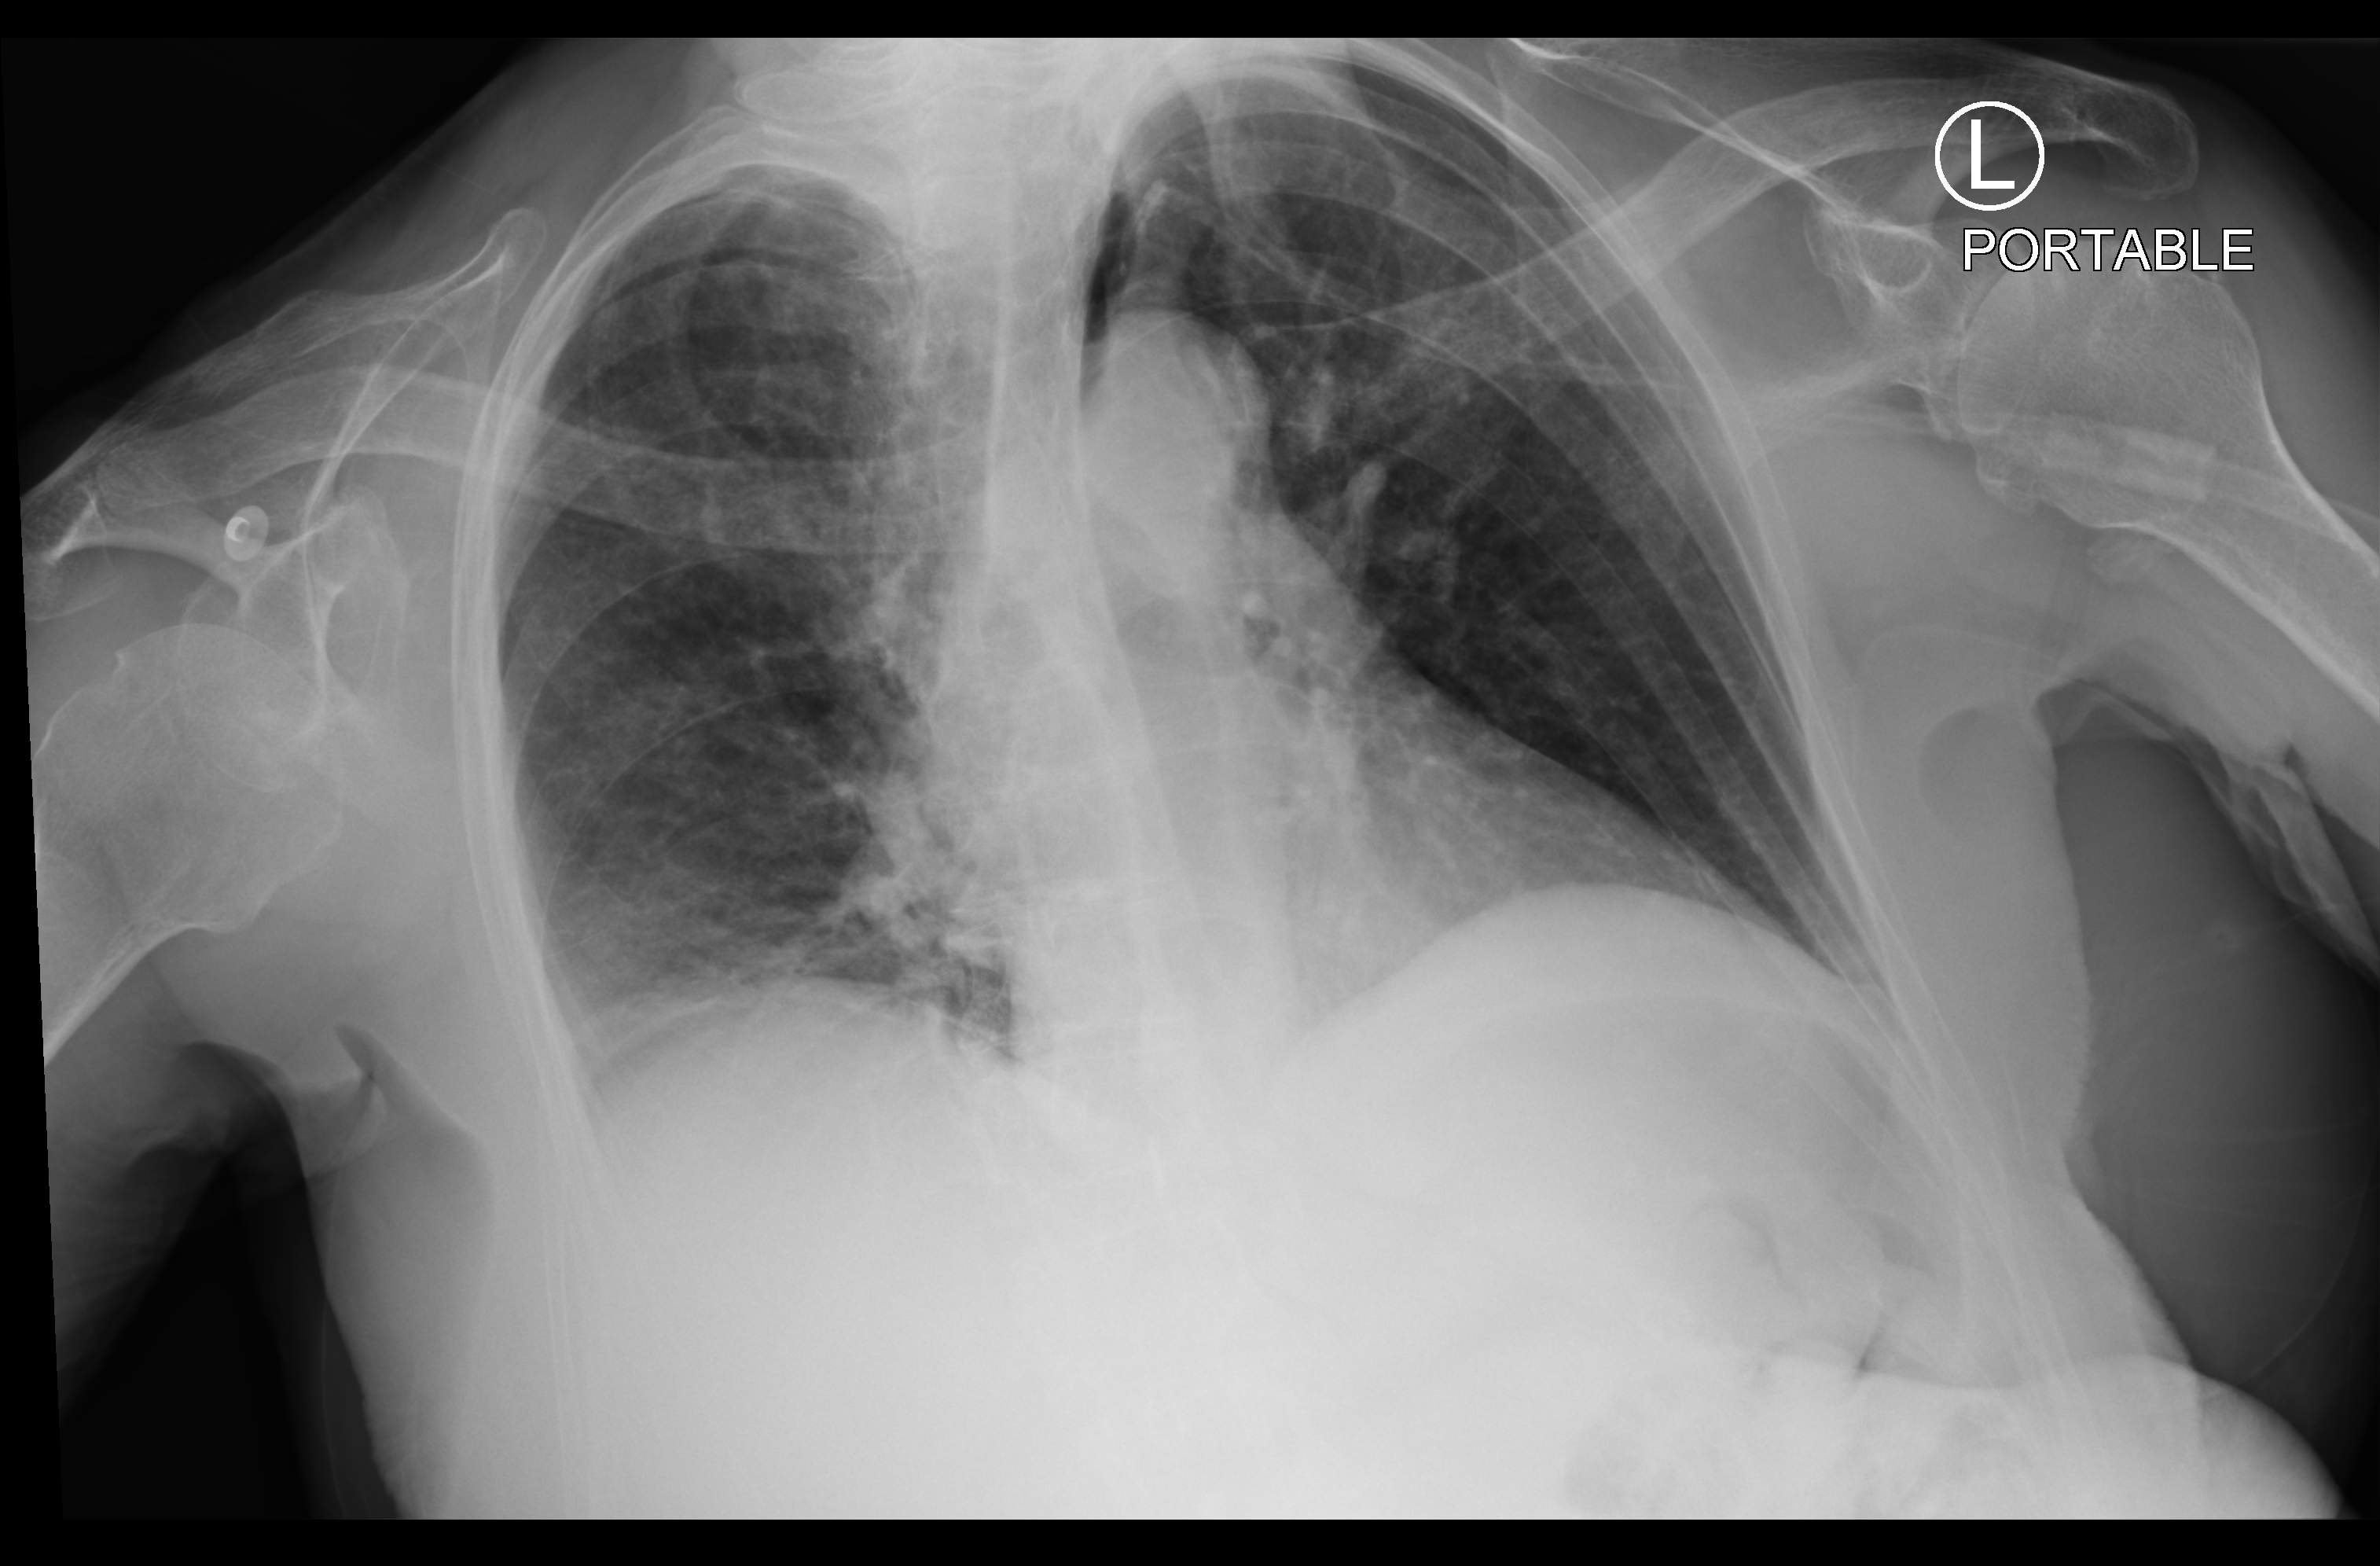
Chest X-ray (portable). Female patient hospitalised with COVID-19, age 60–74 years.
Admission-level facts for this patient (not findings on this image; timing relative to this image not recorded):
- admitted to intensive care during this hospital stay: no
- mechanically ventilated during this hospital stay: no